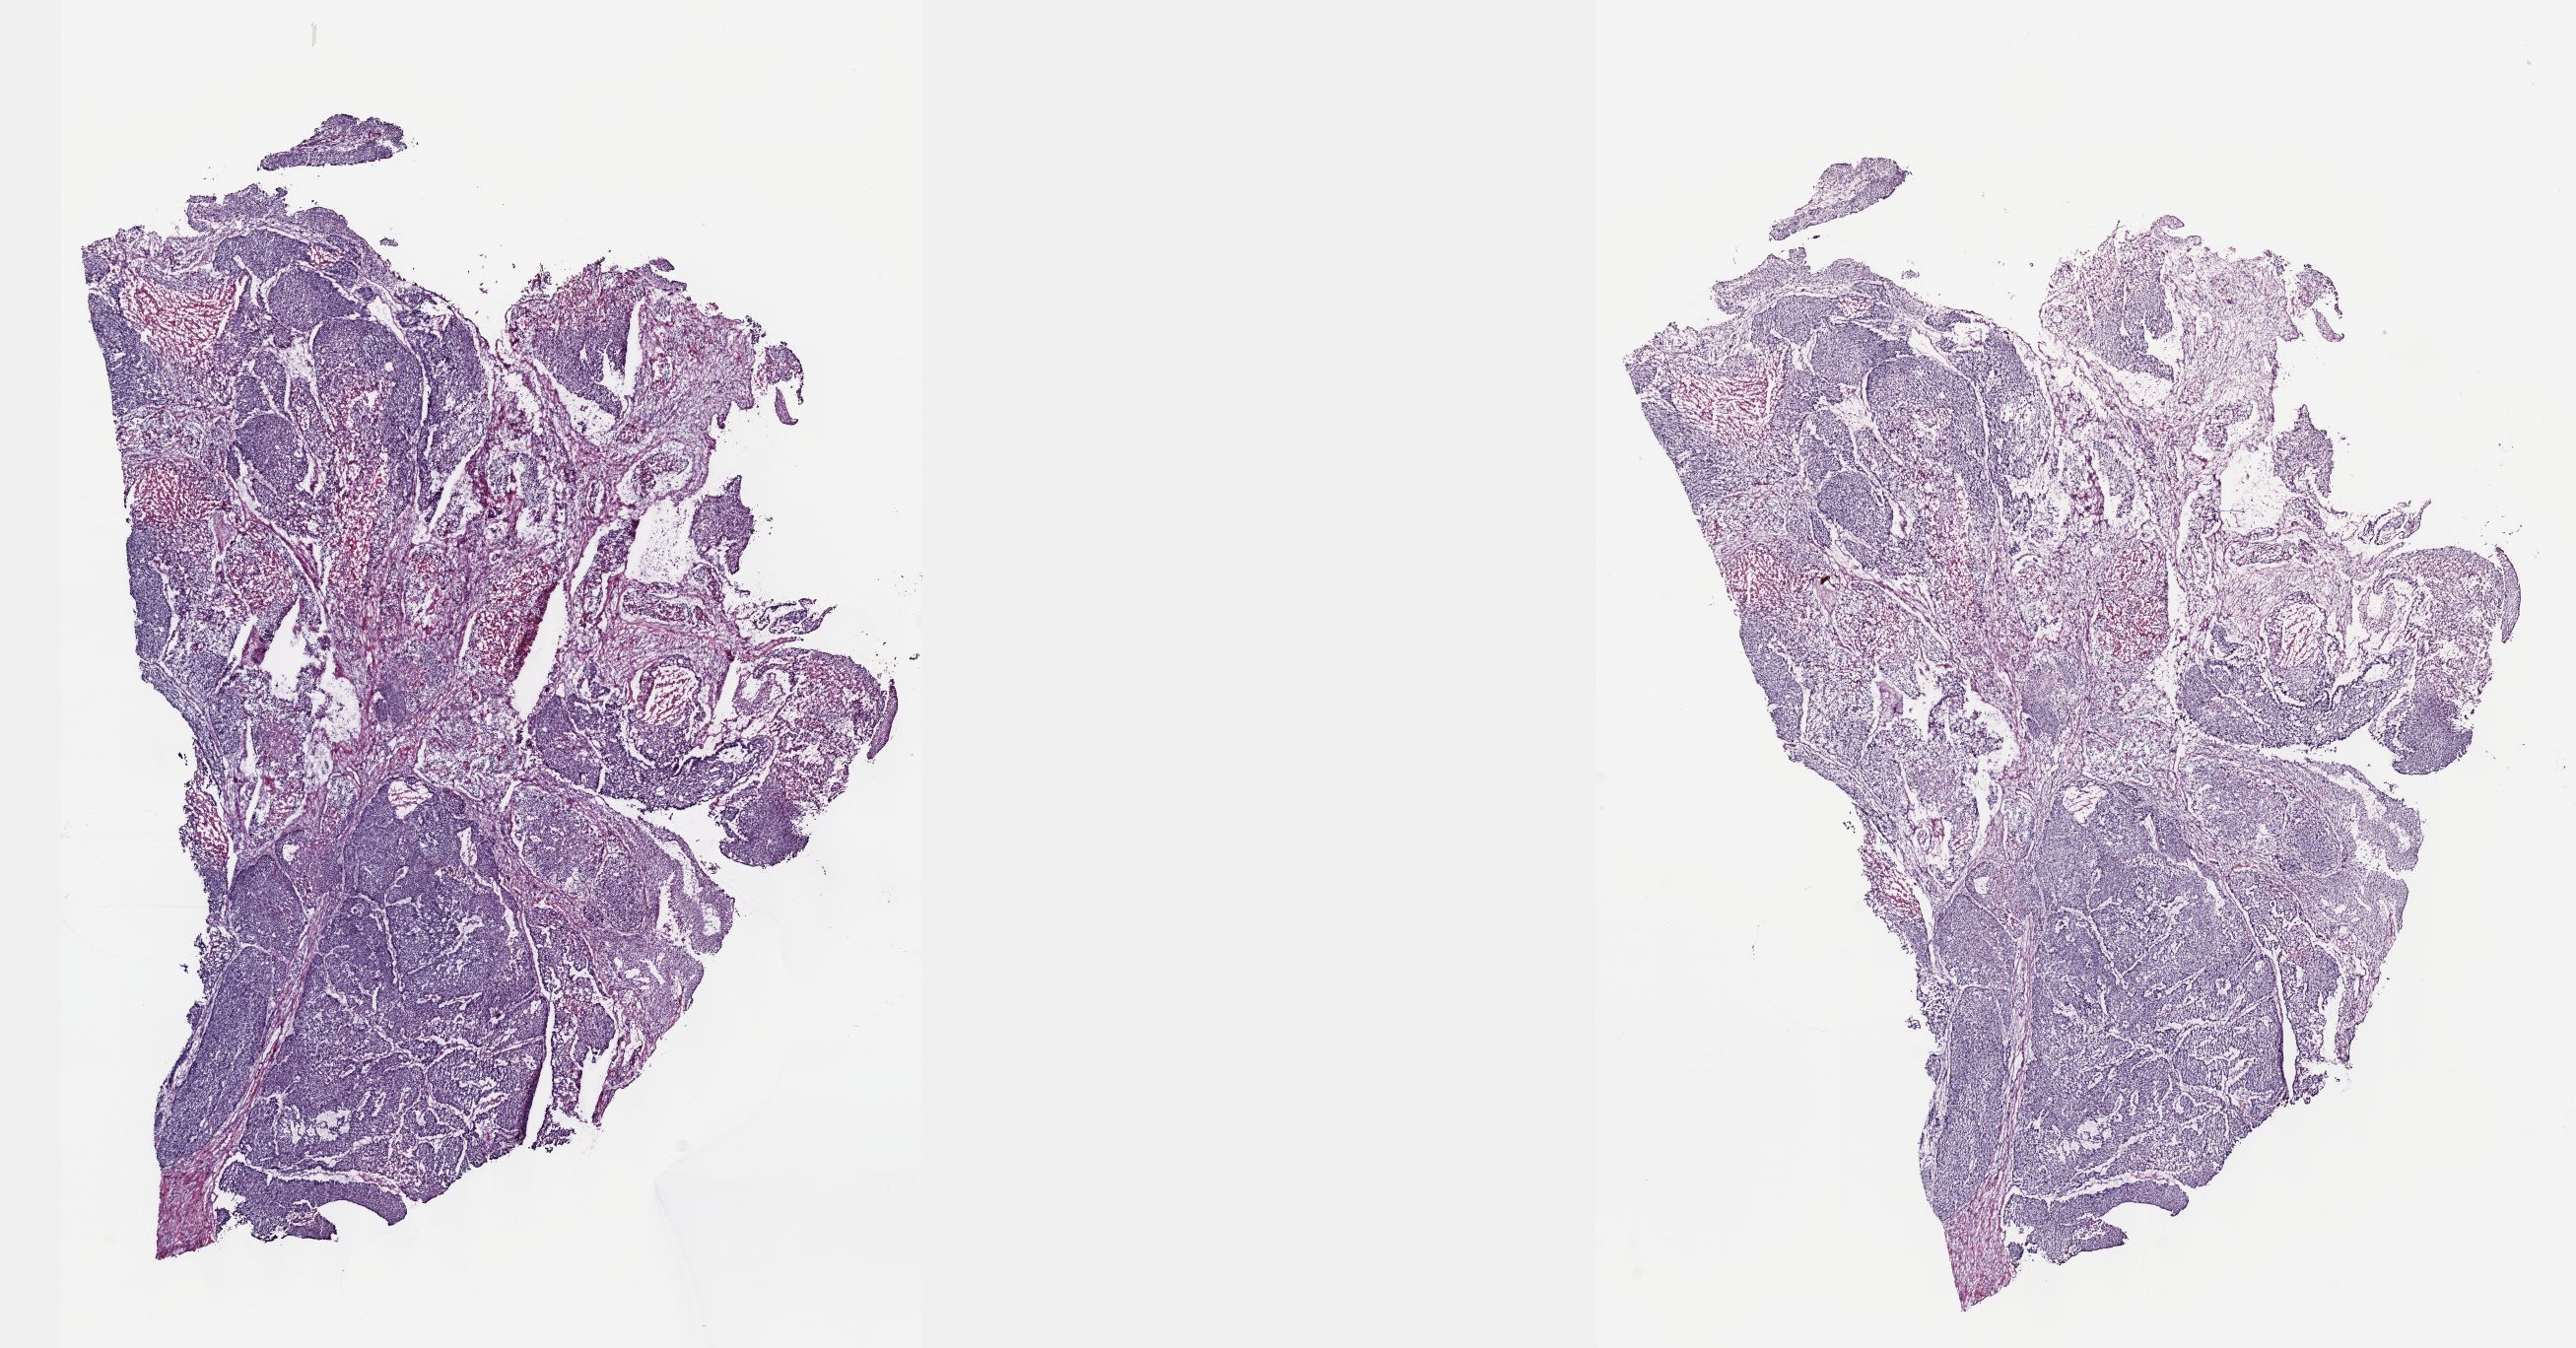
Hematoxylin and eosin (H&E) stained whole-slide image, low-resolution overview of the scanned area, about 21.1 x 11.1 mm, frozen section, bladder, primary tumour sample. Male patient; age at initial diagnosis 80 years. Histologic grade: high grade. Composition of this section per pathologist review: tumour cells 65%, tumour nuclei 75%, normal cells 0%, stromal cells 25%, necrosis 10%. Infiltration values recorded for this section: lymphocyte infiltration 0%, monocyte infiltration 0%, neutrophil infiltration 0%.
AJCC pathologic stage: IV (6th edition). TNM: T3b N1 MX. Lymph nodes positive (case pathology): 4 of 43 examined. Diagnosis: Transitional cell carcinoma.